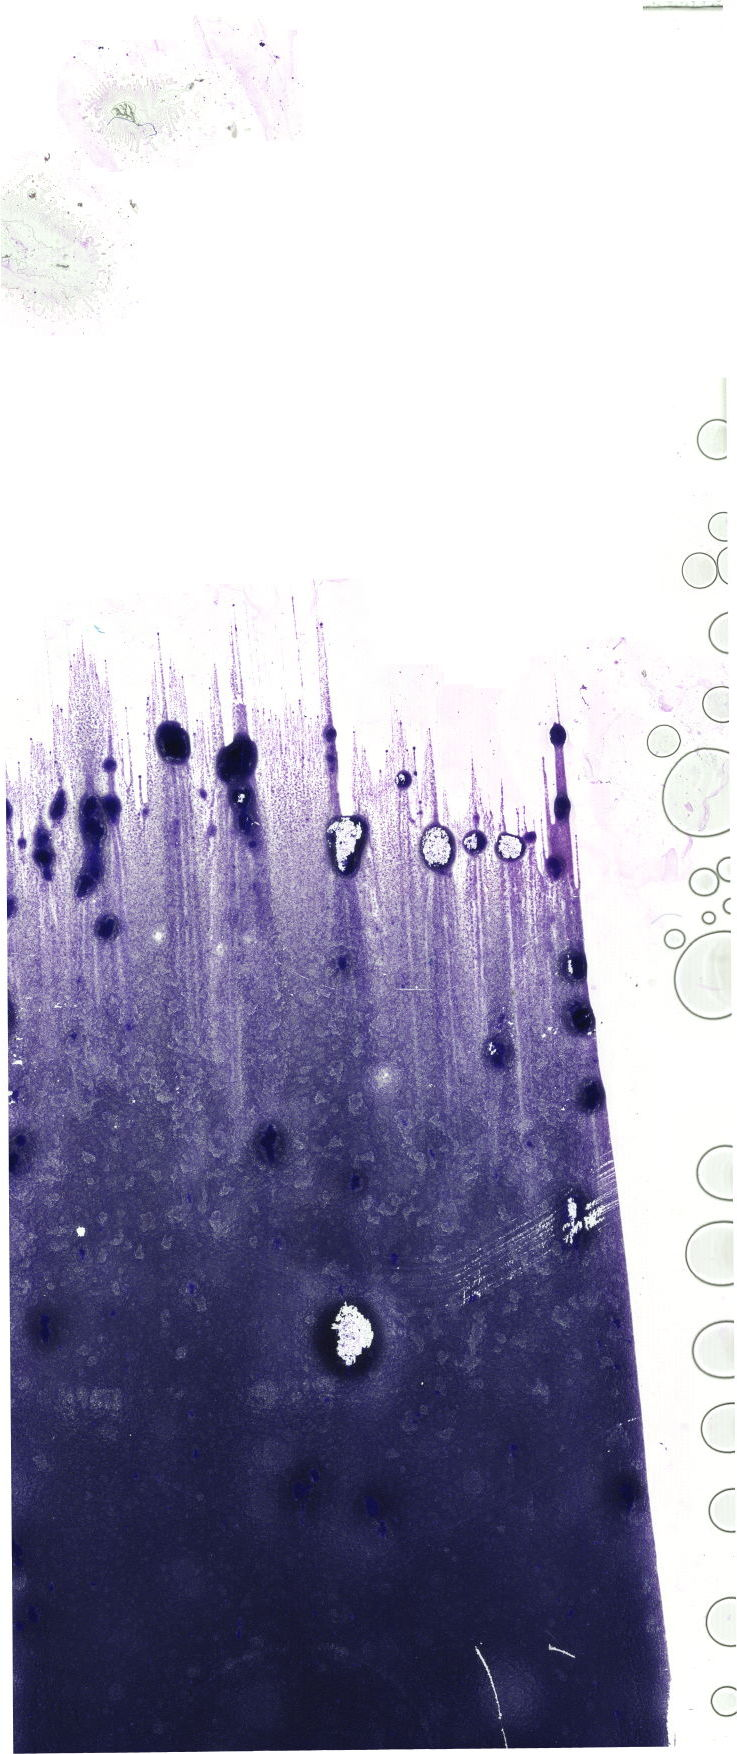
Whole-slide image of a May-Grünwald–Giemsa-stained bone marrow aspirate smear, low-resolution overview of the scanned area, about 20.9 x 49.7 mm. Male patient.
Diagnosis: Chronic Phase Chronic Myeloid Leukemia, BCR-ABL1 Positive.